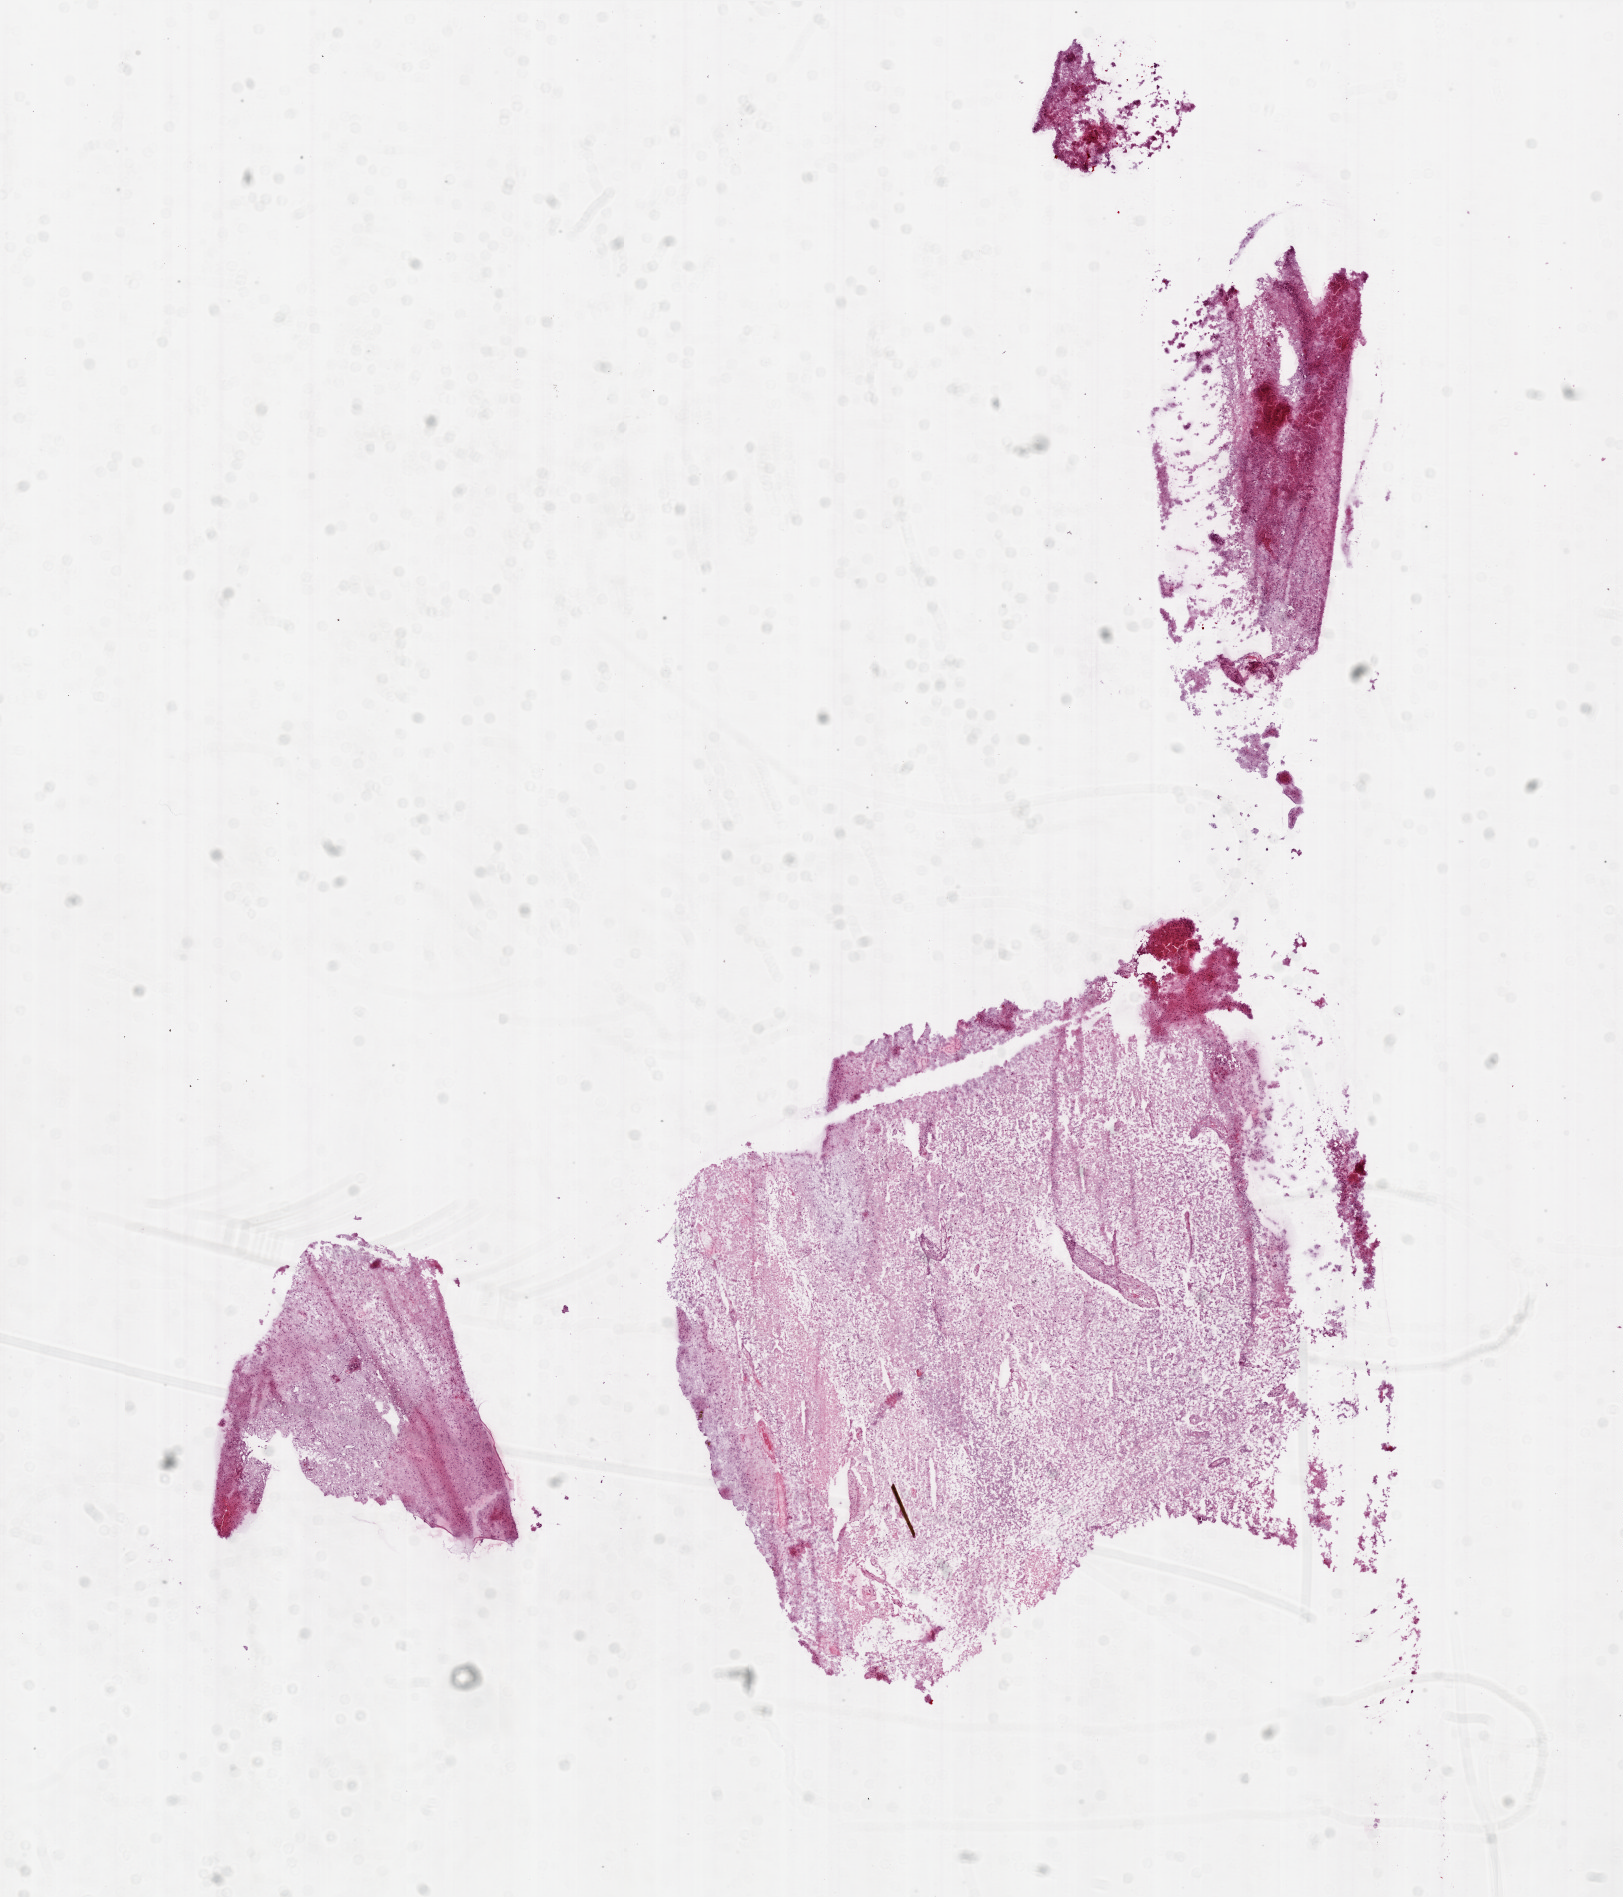
Whole-slide histology image, Hematoxylin and eosin (H&E) stained, shown as a low-resolution overview of the whole scanned area (about 13.0 x 15.2 mm, slide scanned at 20x); frozen section; primary tumour sample from the brain. Female patient; age at initial diagnosis 81 years. Composition of this section per pathologist review: tumour cells 20%, tumour nuclei 85%, normal cells 0%, stromal cells 0%, necrosis 80%. Inflammatory infiltration, as recorded: lymphocyte infiltration 0%, monocyte infiltration 0%, neutrophil infiltration 100%.
Pathologic diagnosis: Glioblastoma.